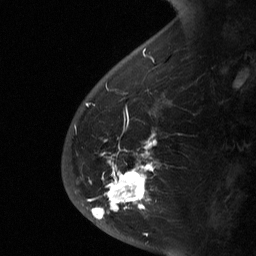
Breast MRI (dynamic contrast-enhanced), one sagittal slice. Slice 17 of 64 in the series (ordered by position). Dynamic contrast-enhanced study with each time point stored as its own series, time point 2 of 3 at this slice position (early post-contrast, ordered by acquisition time). 1.5 T. TE 4.8 ms, TR 27 ms. 256 × 256 image matrix, field of view 180 × 180 mm. Female patient, age 56 years. From the clinical record (not read from this slice): setting: breast cancer imaged before/during neoadjuvant chemotherapy; receptor status: HER2-positive.
Structures marked on this image (semi-automatic segmentation, software-assisted and operator-edited):
- analysis volume of interest (the breast-tissue region the enhancement analysis was run in; not a lesion): box from (x=62, y=134) to (x=181, y=229) px
- tumour enhancement mask (voxels above the 90 % enhancement threshold inside the analysis volume of interest): (x=87, y=134)–(x=156, y=219)